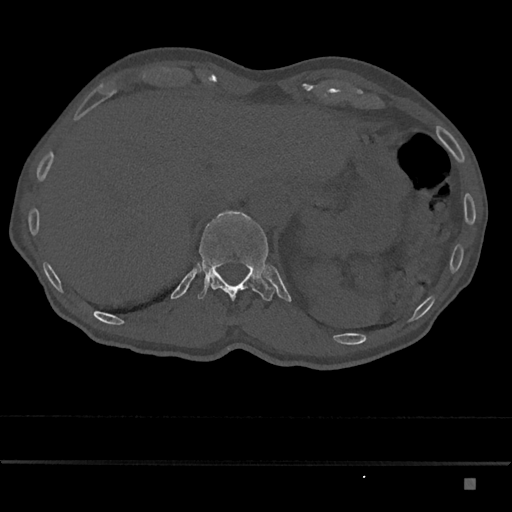
CT including the spine, one axial slice. Reconstruction kernel Br40s/3. 120 kVp. Bone window (W 1800 / L 400 HU). 0.5 mm slice thickness. 512 × 512 image matrix, field of view 390 × 390 mm. Patient: male, 72 years. From the clinical record (not read from this slice): primary cancer: prostate.
Outlined on this slice (semi-automatically segmented with operator editing):
- T12 vertebra: bounding box [x1, y1, x2, y2] px = [197, 211, 275, 301]